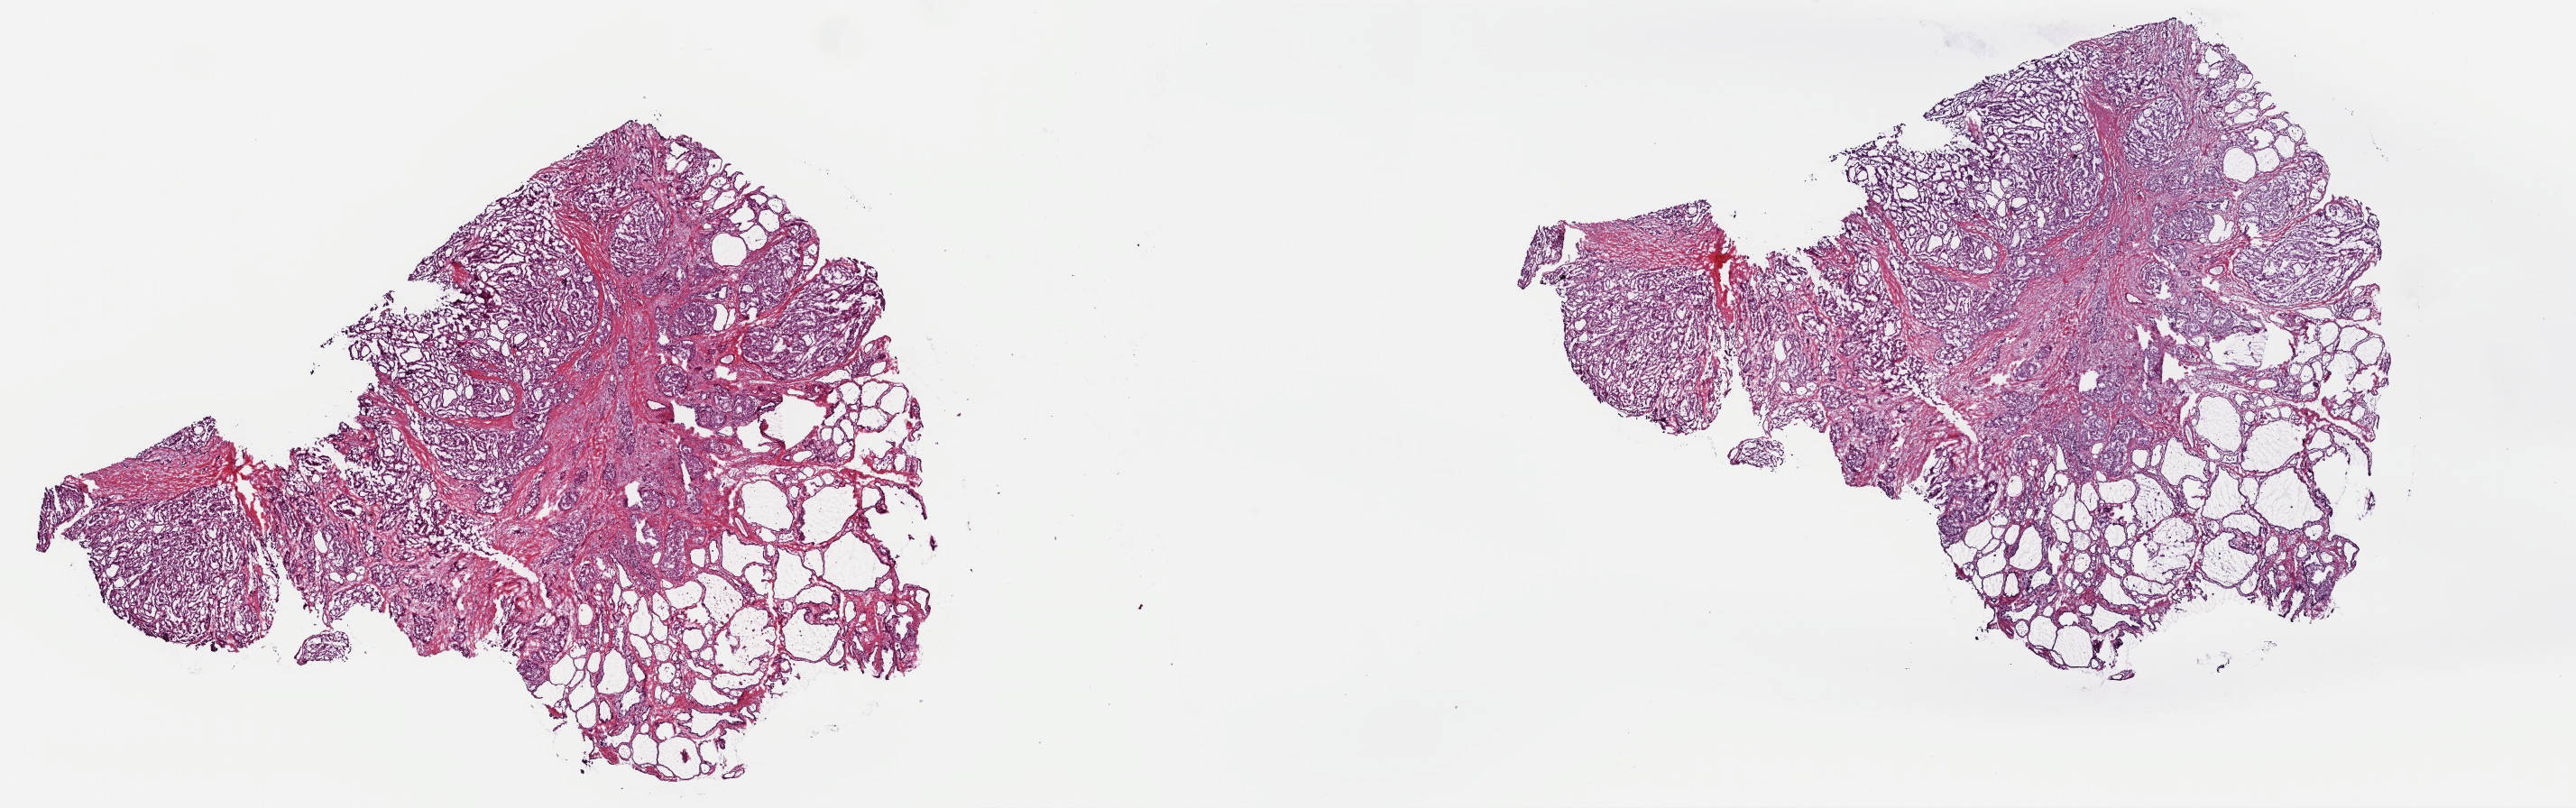
H&E-stained whole-slide image, shown as a low-resolution overview of the whole scanned area (about 22.6 x 7.1 mm). Frozen section from the top of the tissue portion. Primary tumour sample from the thyroid. Patient: female, age at initial diagnosis 18 years. Slide review estimates, as recorded: tumour cells 65%, tumour nuclei 75%, normal cells 35%, stromal cells 0%, necrosis 0%. Infiltration values recorded for this section: lymphocyte infiltration 0%, monocyte infiltration 0%, neutrophil infiltration 0%.
Pathologic diagnosis: Papillary adenocarcinoma, NOS. Lymph nodes positive (case pathology): 0 of 2 examined. AJCC pathologic stage: I (7th edition).